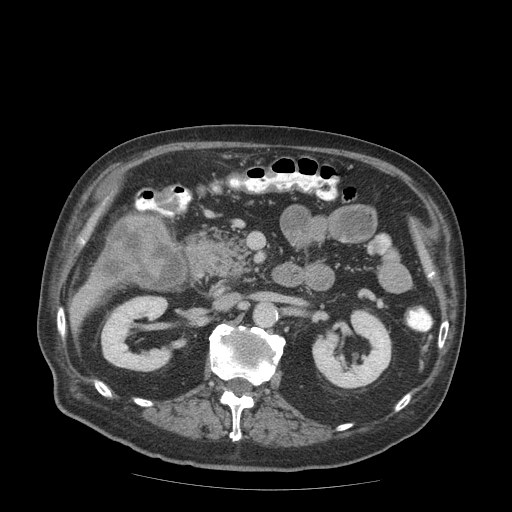
Contrast-enhanced abdominal CT (liver protocol), one axial slice; slice 25 of 99 in the series (ordered by position); soft-tissue window (W 400 / L 40 HU); 2.5 mm slice thickness; 512 × 512 image matrix. Case-level facts recorded for this patient, not image findings: diagnosis: hepatocellular carcinoma (patient treated with transarterial chemoembolisation; whether this scan precedes or follows treatment is not stated here); TNM stage (as recorded): Stage-IIIB; Child-Pugh class: A; tumour differentiation: well differentiated; tumour nodularity: multinodular.
Outlined on this slice (semi-automatic segmentation, software-assisted and operator-edited):
- liver parenchyma outside the tumour (the mass and vessels are separate outlines, so this box may not span the whole liver): bounding box <94,223,180,284> (left, top, right, bottom; pixels)
- mass: <95,214,169,280>